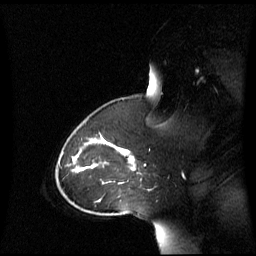
Breast MRI (dynamic contrast-enhanced), one sagittal slice; position 44 of 60 along the scan axis; dynamic contrast-enhanced series, image 2 of 3 at this slice position (ordered by acquisition); 1.5 T; TE 4.2 ms, TR 8.4 ms; 2.8 mm slice thickness; 256 × 256 image matrix. Patient: female, 43 years. Case-level facts recorded for this patient, not image findings: setting: breast cancer imaged before/during neoadjuvant chemotherapy; receptor status: triple-negative.
Outlined on this slice (semi-automatically segmented with operator editing):
- analysis volume of interest (the breast-tissue region the enhancement analysis was run in; not a lesion): bounding box <69,137,142,198> (left, top, right, bottom; pixels)
- tumour enhancement mask (voxels above the 70 % enhancement threshold inside the analysis volume of interest): <119,148,134,162>